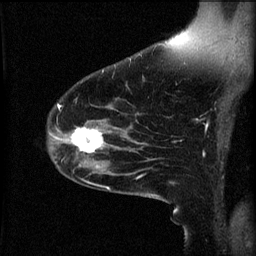
Breast MRI (dynamic contrast-enhanced), one sagittal slice; position 38 of 60 along the scan axis; 3 images stored at this slice position (order not interpretable as contrast timing); 1.5 T; TE 4.2 ms, TR 8.2 ms; 256 × 256 image matrix, field of view 200 × 200 mm. Female patient, age 49 years.
Structures marked on this image (semi-automatically segmented with operator editing):
- analysis volume of interest (the breast-tissue region the enhancement analysis was run in; not a lesion): bounding box (x1, y1, x2, y2) in pixels: (66, 124, 113, 159)
- tumour enhancement mask (voxels above the 70 % enhancement threshold inside the analysis volume of interest): (66, 128, 107, 153)